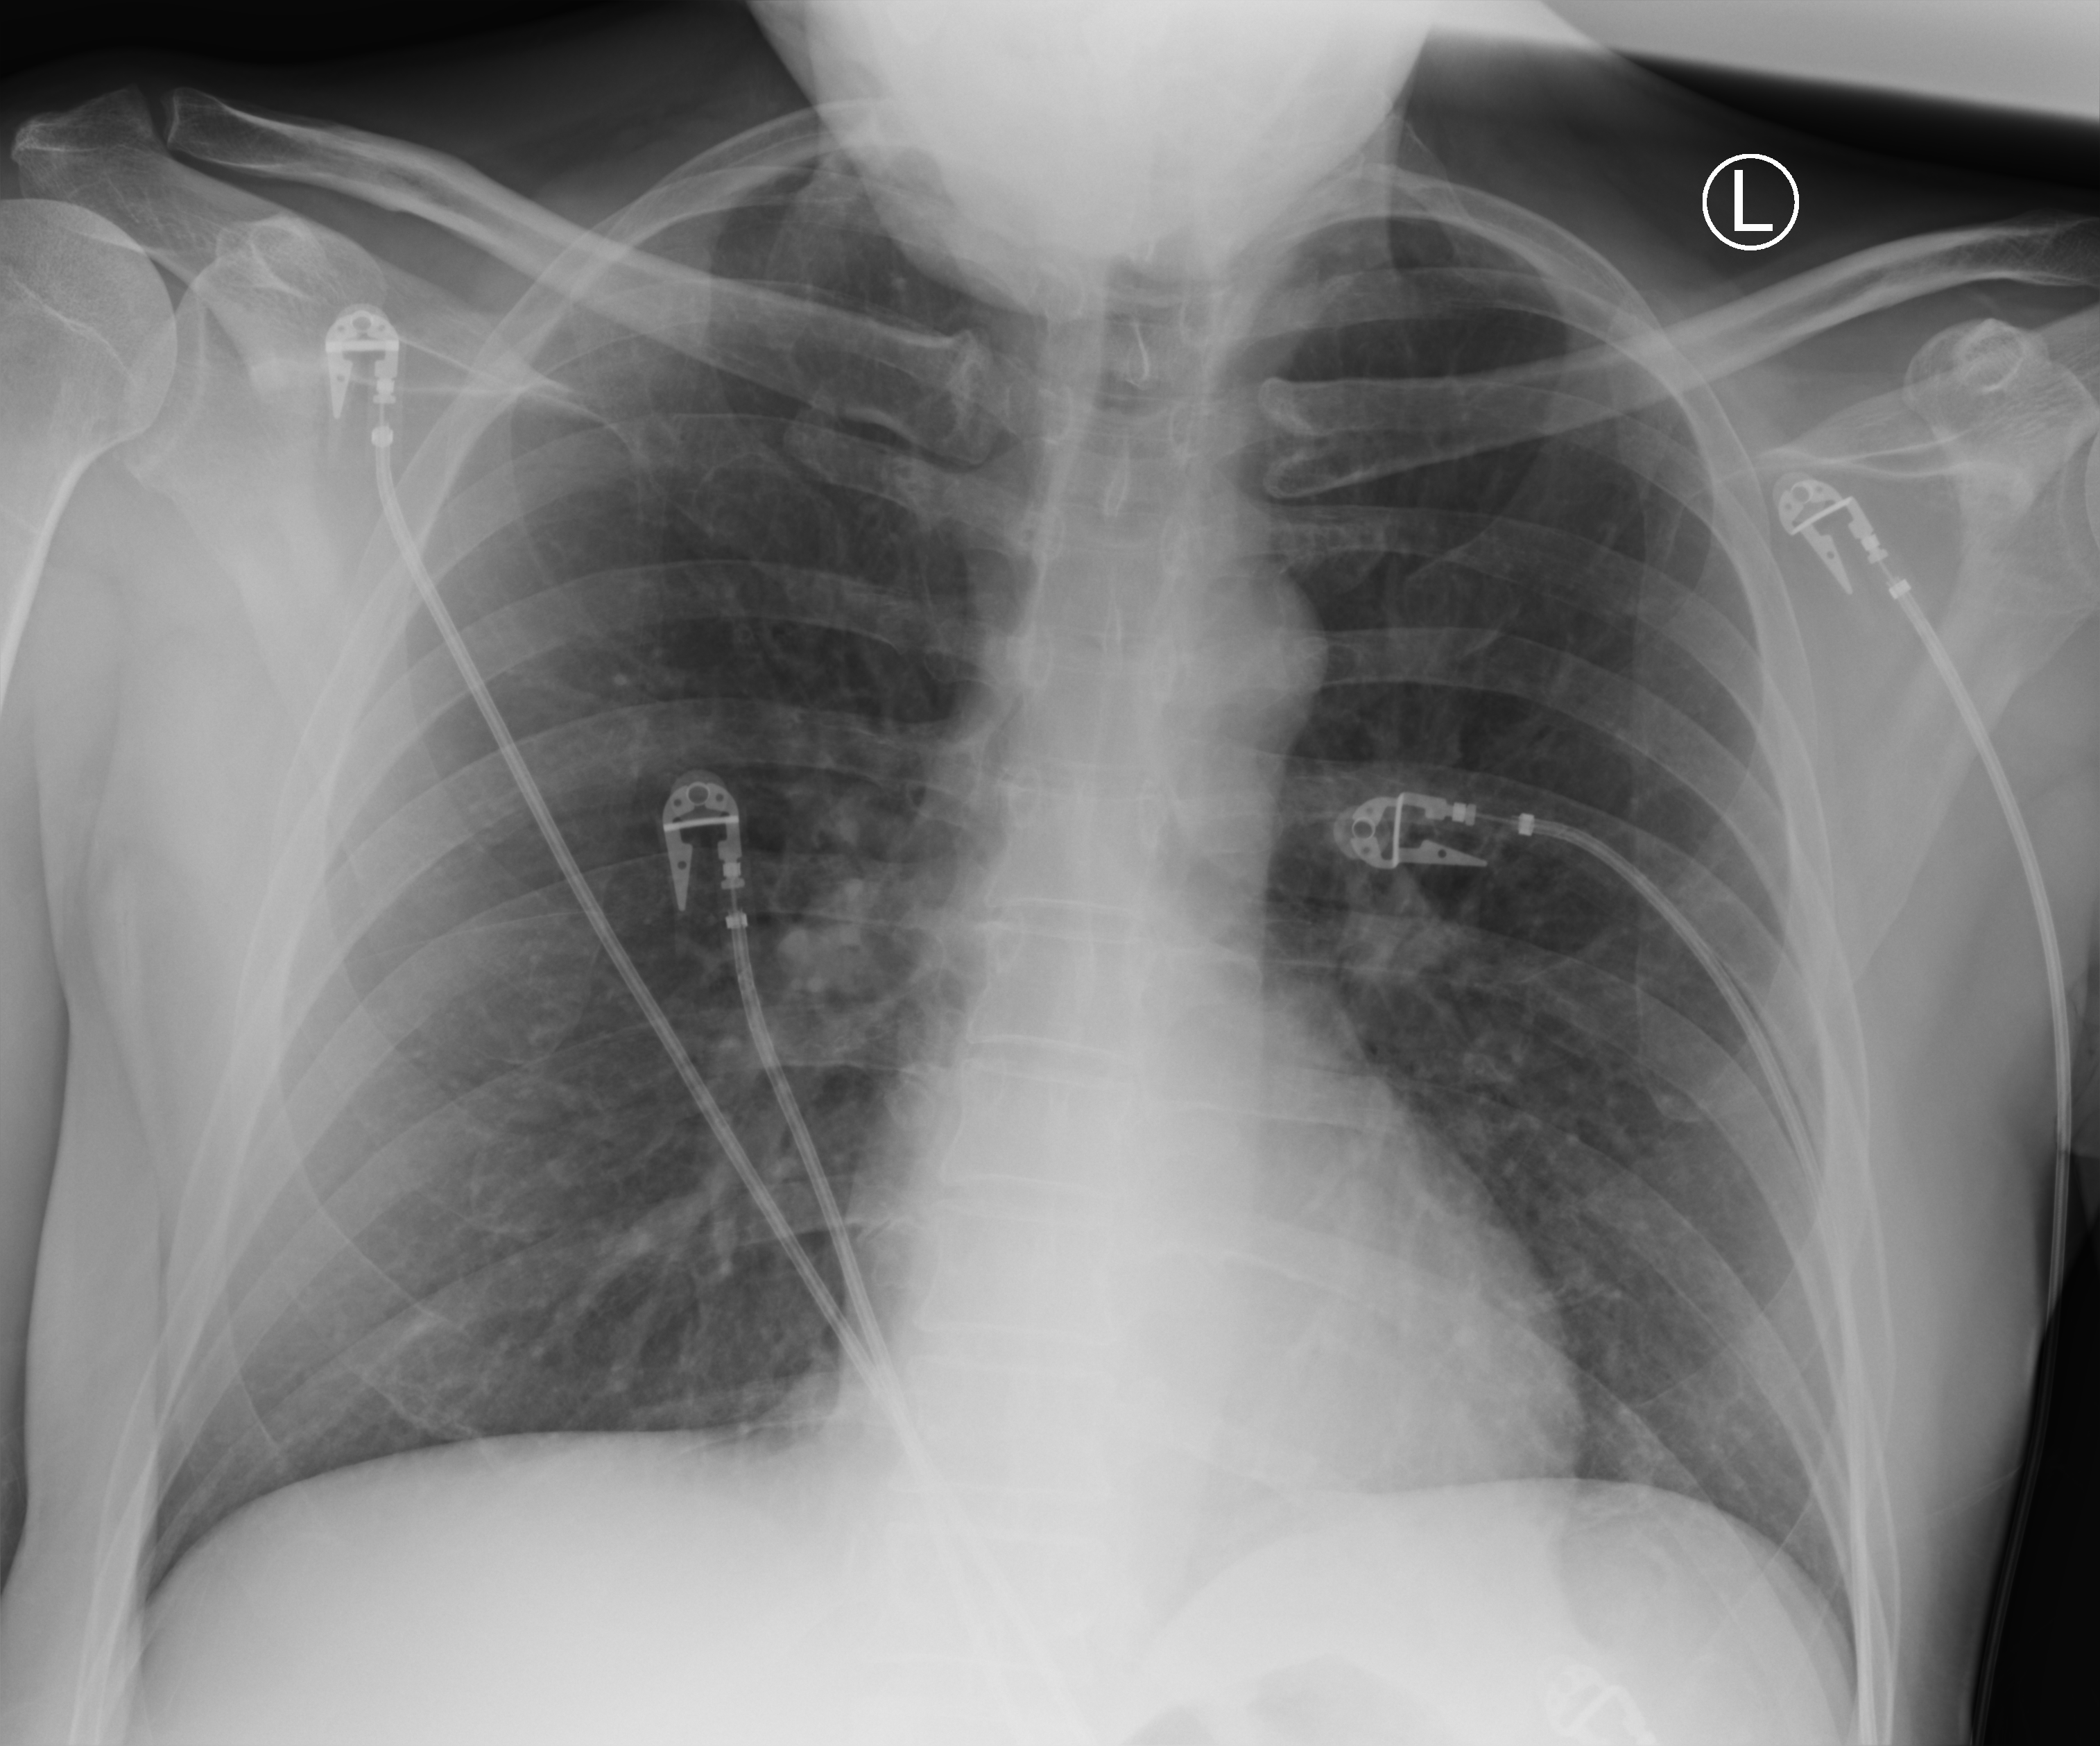
Chest X-ray (portable); anteroposterior (AP) projection. Male patient hospitalised with COVID-19, age 18–59 years.
Admission-level facts for this patient (not findings on this image; timing relative to this image not recorded):
- mechanically ventilated during this hospital stay: no